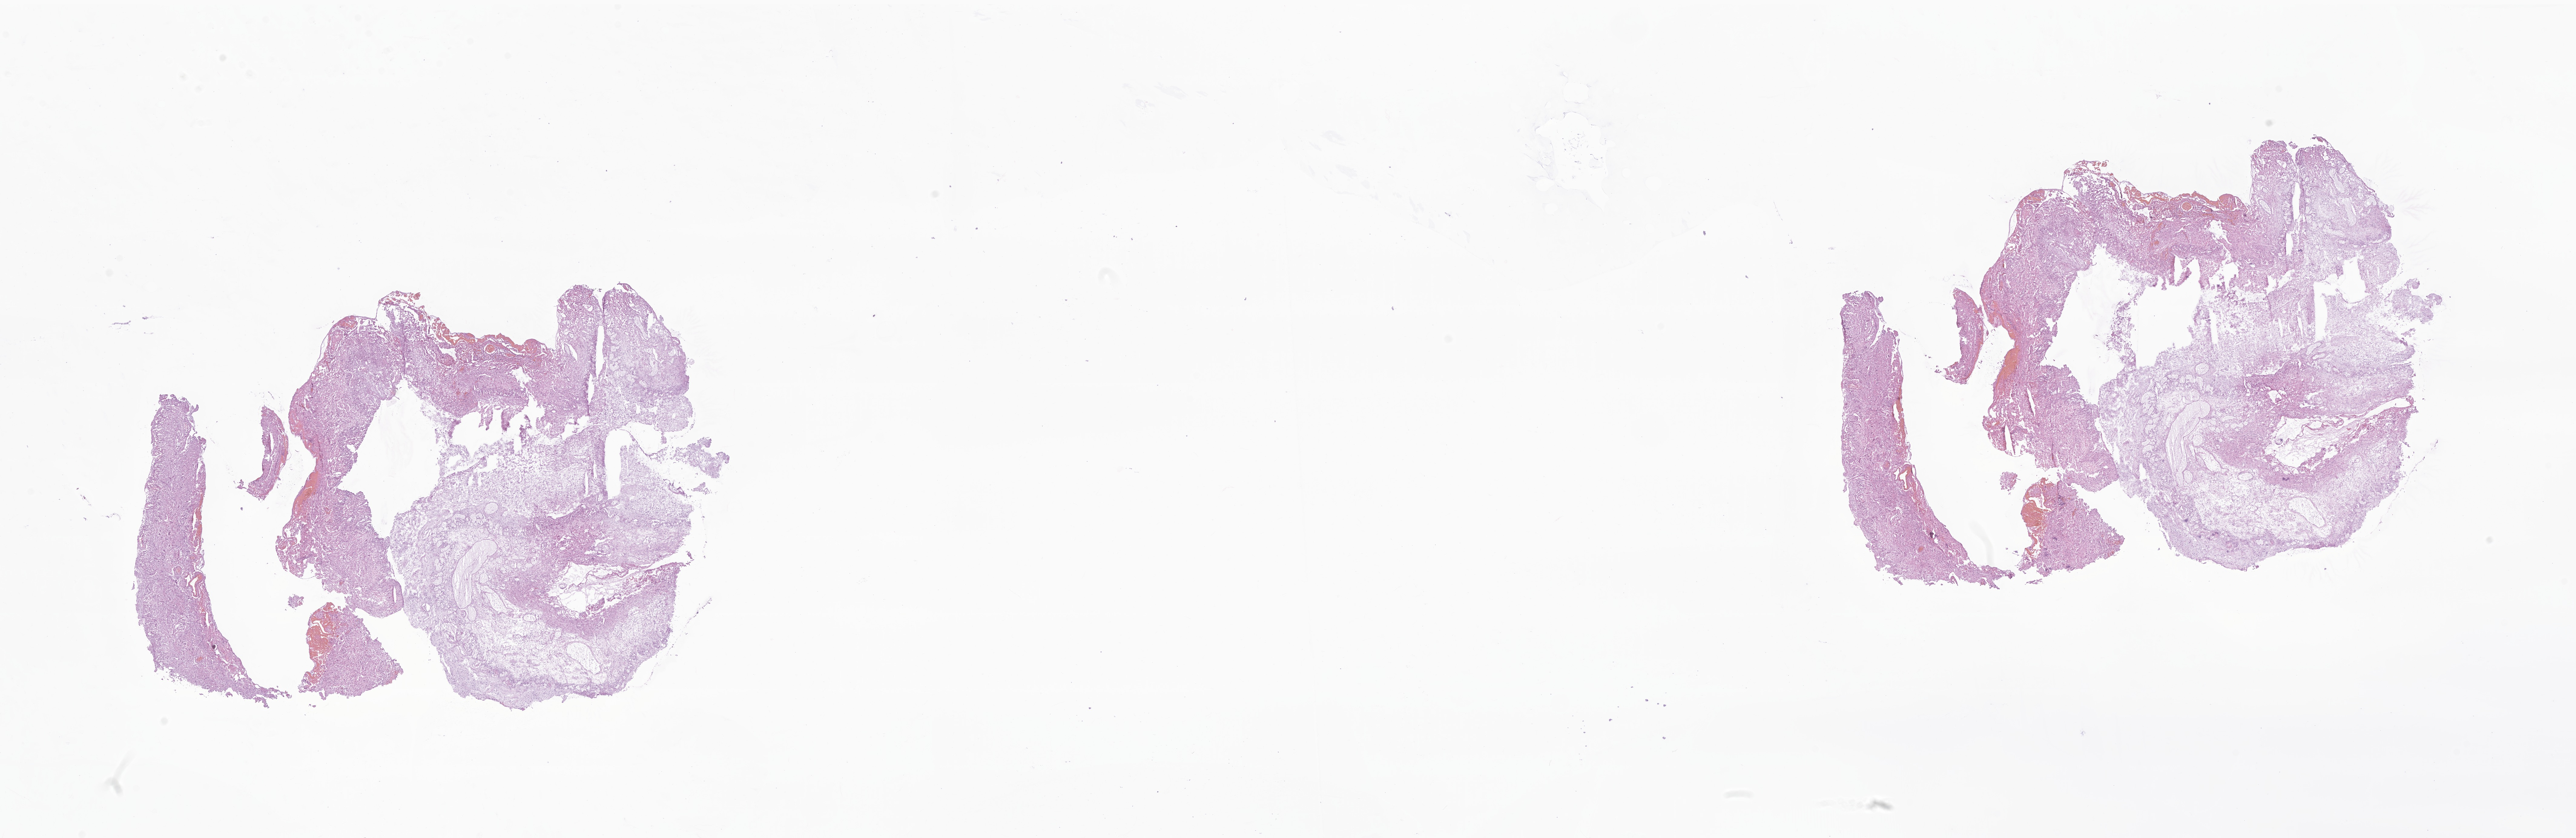
Whole-slide image, hematoxylin and eosin (H&E) stain of tumor tissue from the brain, a low-resolution overview of the entire scanned area, about 35.9 x 11.7 mm; frozen section (OCT-embedded). Patient: female, age 172 months (14 years 4 months).
Diagnosis: Glioma, malignant.